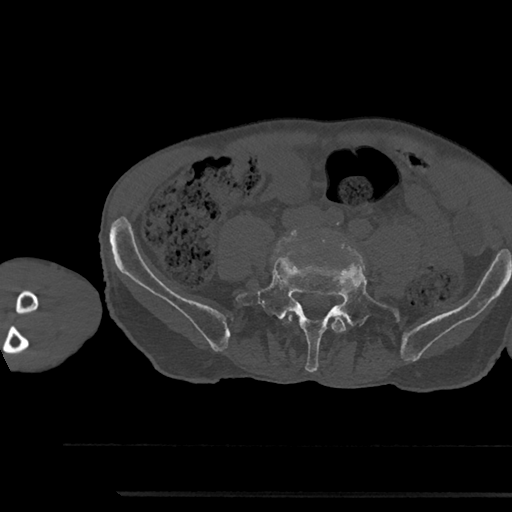
CT including the spine, one axial slice. Position 362 of 797 along the scan axis. 120 kVp. Bone window (W 1800 / L 400 HU). 512 × 512 image matrix. Patient: male, 79 years. From the clinical record (not read from this slice): primary cancer: prostate.
Structures marked on this image (semi-automatically segmented with operator editing):
- L4 vertebra: bounding box (x1, y1, x2, y2) in pixels: (285, 315, 346, 333)
- L5 vertebra: (235, 256, 400, 372)